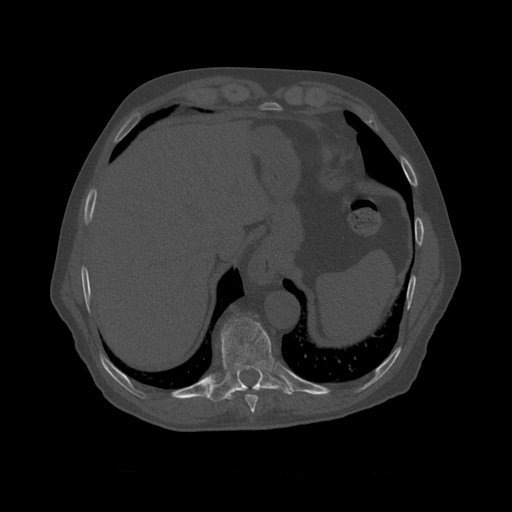
CT including the spine, one axial slice. Position 430 of 450 along the scan axis. Reconstruction kernel STANDARD. Bone window (W 1800 / L 400 HU). 1.25 mm slice thickness. 512 × 512 image matrix, field of view 405 × 405 mm. Patient age 75 years. From the clinical record (not read from this slice): primary cancer: prostate.
Annotated regions visible in this slice (semi-automatically segmented with operator editing):
- T8 vertebra: box from (x=245, y=391) to (x=258, y=410) px
- T9 vertebra: (x=213, y=316)–(x=292, y=400)